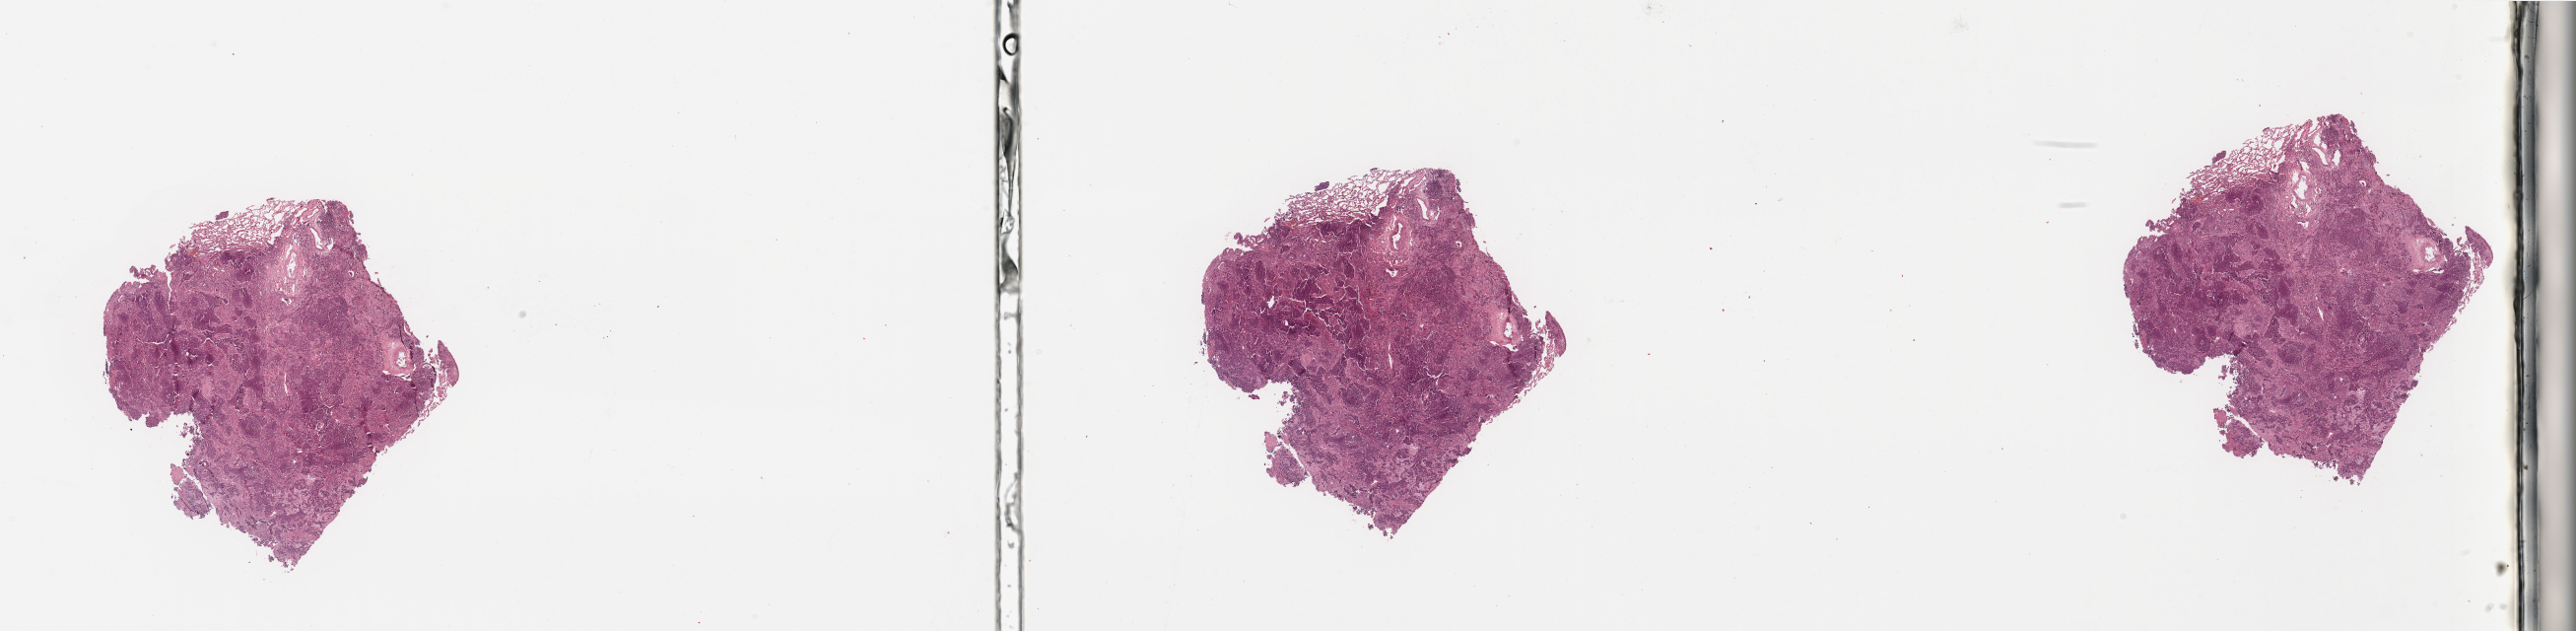
H&E whole-slide image, low-resolution overview of the scanned area, about 41.3 x 10.1 mm (acquisition: 20x scan). Tumour tissue sample, sampled site: lung. 54-year-old male patient. Histologic grade: G2 (moderately differentiated). Slide review estimates, as recorded: tumour nuclei 65%, necrosis 3%.
* primary tumour site (as recorded): left upper lobe
* AJCC pathologic stage: IA
* histologic diagnosis: Adenocarcinoma, NOS